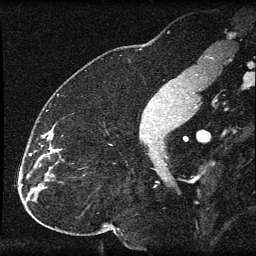
Breast MRI (dynamic contrast-enhanced), one sagittal slice; slice 32 of 60 in the series (ordered by position); dynamic contrast-enhanced series, image 2 of 3 at this slice position (ordered by acquisition); 1.5 T; TE 4.2 ms, TR 8.2 ms; 256 × 256 image matrix, field of view 180 × 180 mm. Patient: female, 32 years.
Annotated regions visible in this slice (semi-automatic segmentation, software-assisted and operator-edited):
- analysis volume of interest (the breast-tissue region the enhancement analysis was run in; not a lesion): bounding box <32,129,64,184> (left, top, right, bottom; pixels)
- tumour enhancement mask (voxels above the 70 % enhancement threshold inside the analysis volume of interest): <44,133,59,152>